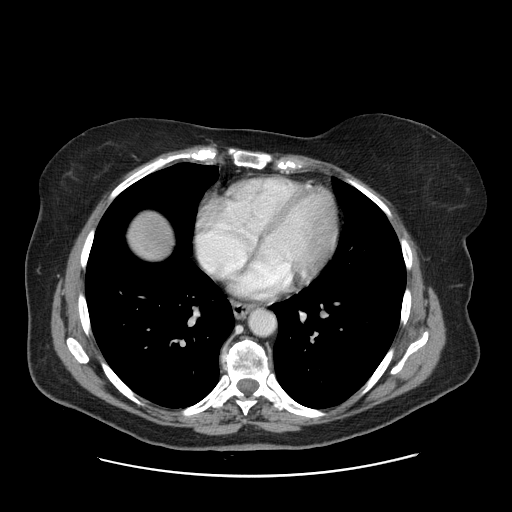
Contrast-enhanced abdominal CT, one axial slice; slice 155 of 161 in the series (ordered by position); 120 kVp; intravenous contrast given; soft-tissue window (W 400 / L 40 HU); 2.5 mm slice thickness; 512 × 512 image matrix, field of view 398 × 398 mm. Female patient, age 62 years. From the clinical record (not read from this slice): diagnosis: colorectal cancer liver metastases, imaged before liver resection; multiple liver metastases: no; largest metastasis: 2.5 cm; disease in both lobes: no.
Annotated regions visible in this slice (outlined manually by an expert reader):
- liver: bounding box [x1, y1, x2, y2] px = [130, 213, 172, 259]
- planned liver remnant (the part of the liver to remain after resection): [130, 214, 172, 259]